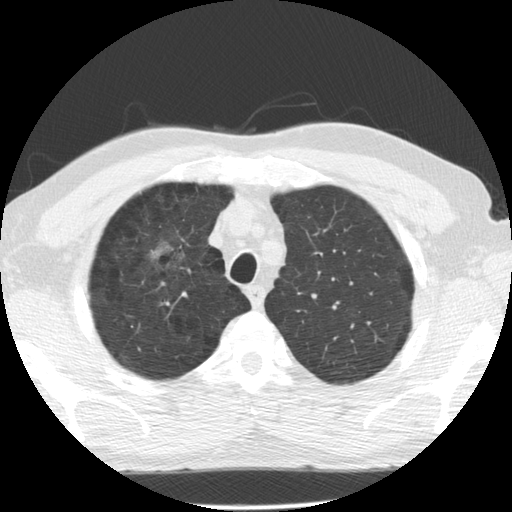
Chest CT (low-dose screening protocol), one axial image, second annual screen, lung window (W 1500 / L -600 HU), 2.5 mm slice thickness, standard (soft-tissue) reconstruction kernel (STANDARD), 512 × 512 image matrix, field of view 350 × 350 mm. Male, age 60 years at enrolment. Former smoker at enrolment.
• Lesion marked by an expert reader, bounding box (x1, y1, x2, y2) in pixels: (134, 233, 189, 291).
• The exam's reader record, not a measurement of the box and not confirmed to be the same lesion: non-calcified nodule or mass ≥4 mm, right upper lobe, poorly defined margins, mixed attenuation, pre-existing on the prior screen: yes; interval growth: yes.
• Official screen result: positive, other.
• Participant outcome: lung cancer diagnosed 562 days after this screen — papillary adenocarcinoma, NOS, right upper lobe, moderately differentiated (G2), stage IB (AJCC 6th edition), 32 mm at pathology.